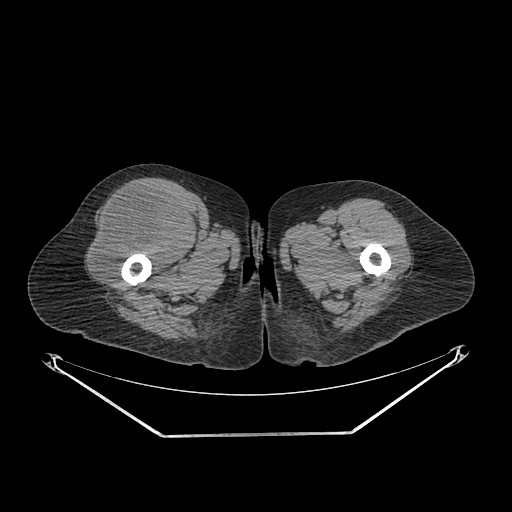
CT of an extremity soft-tissue mass (from a PET/CT study), one axial slice. Slice 266 of 311 in the series (ordered by position). Reconstruction kernel SOFT. Soft-tissue window (W 400 / L 40 HU). 3.75 mm slice thickness. 512 × 512 image matrix, field of view 500 × 500 mm. Female patient. Case-level facts recorded for this patient, not image findings: histological type: pleiomorphic undifferentiated sarcoma; grade: high; site of the primary tumour: right quadricep.
Annotated regions visible in this slice (expert contour drawn on MRI and transferred to this co-registered scan by the dataset authors):
- tumour plus oedema (research contour): box from (x=93, y=189) to (x=186, y=279) px
- tumour (research contour): (x=93, y=189)–(x=186, y=279)